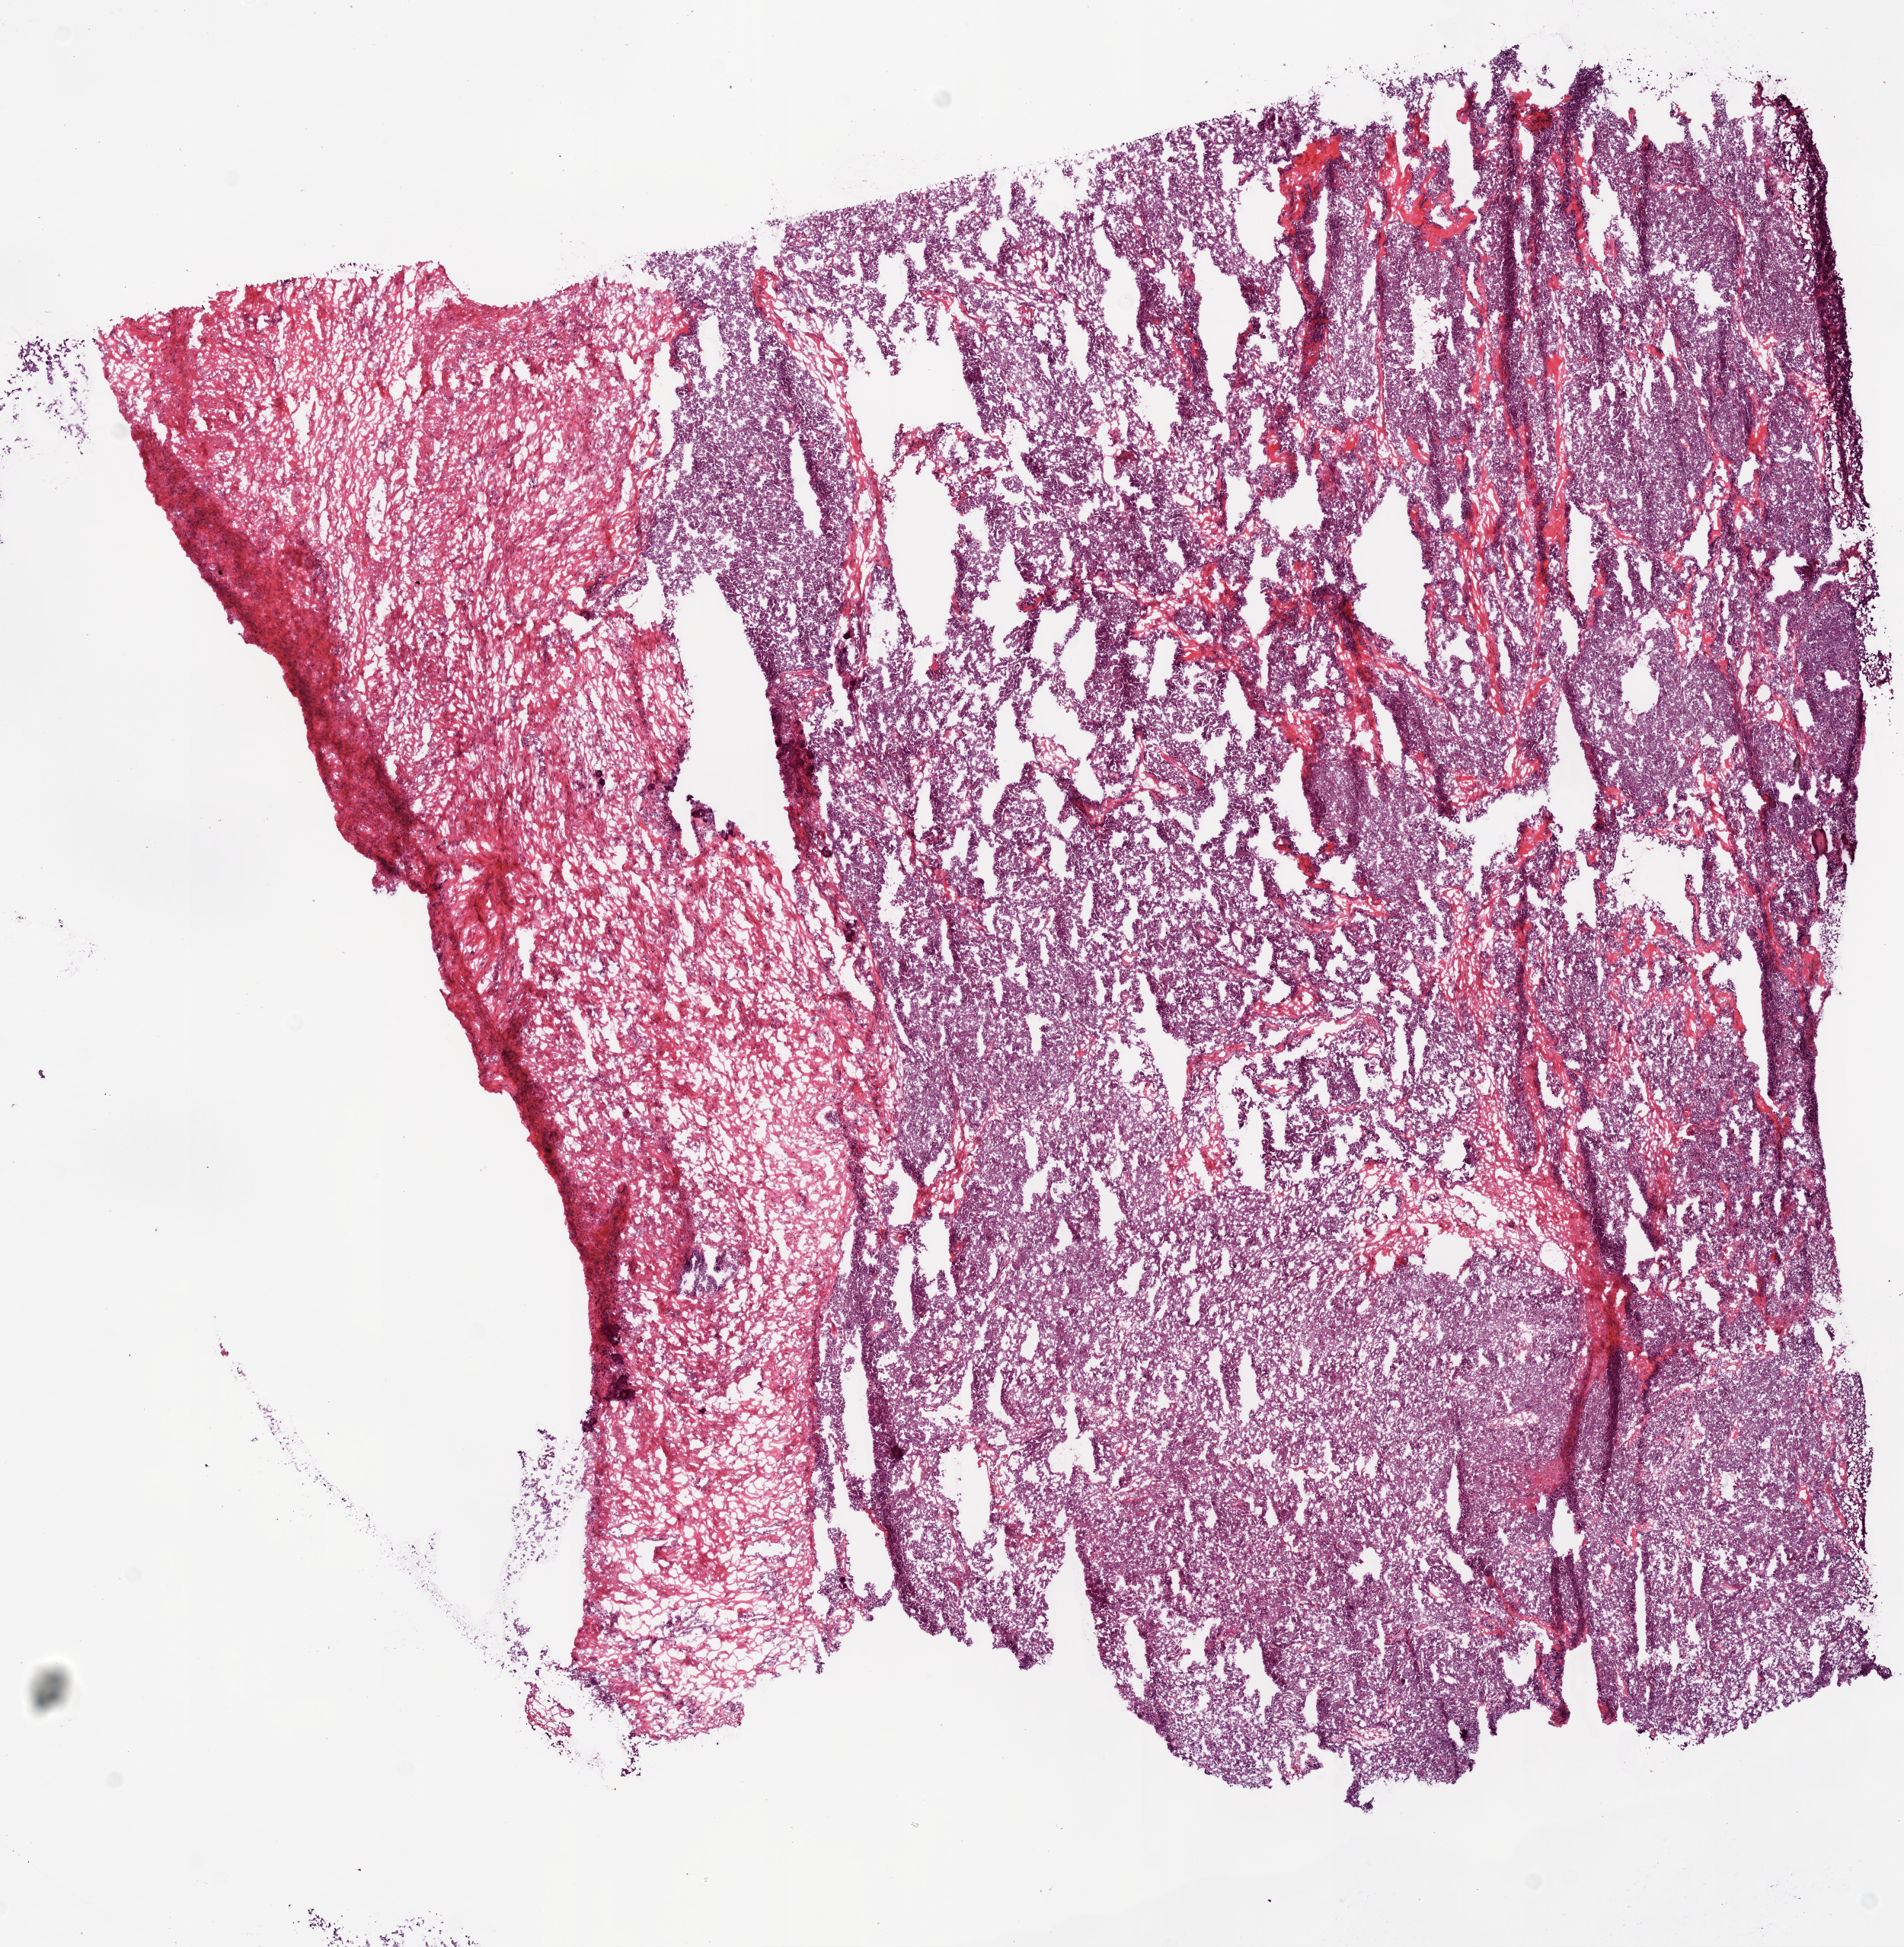
Digitized Hematoxylin and eosin (H&E) stained tissue section (whole slide) — a low-resolution overview of the entire scanned area, about 10.0 x 10.3 mm; frozen section from the bottom of the tissue portion; ovary, primary tumour sample. Female, age 76 years at initial diagnosis. Histologic grade: G2 (moderately differentiated). Slide review estimates, as recorded: tumour cells 75%, tumour nuclei 90%, normal cells 0%, stromal cells 25%, necrosis 0%.
FIGO stage: IIIC. Histologic diagnosis: Serous cystadenocarcinoma, NOS.